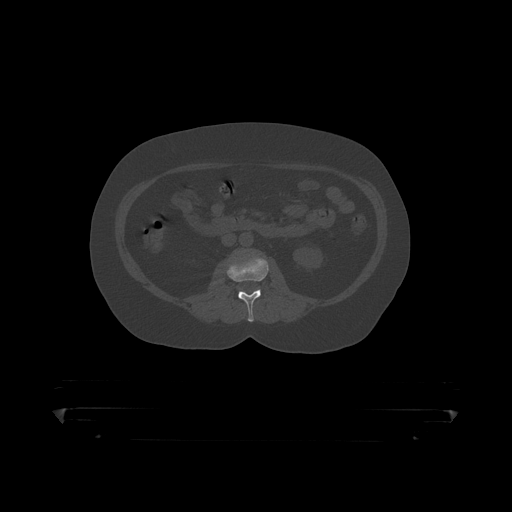
CT including the spine, one axial slice. Slice 110 of 390 in the series (ordered by position). Reconstruction kernel STANDARD. Bone window (W 1800 / L 400 HU). 1.25 mm slice thickness. 512 × 512 image matrix, field of view 650 × 650 mm. Patient: male, 60 years. From the clinical record (not read from this slice): primary cancer: prostate.
Structures marked on this image (semi-automatic segmentation, software-assisted and operator-edited):
- L2 vertebra: bounding box (x1, y1, x2, y2) in pixels: (227, 253, 283, 319)